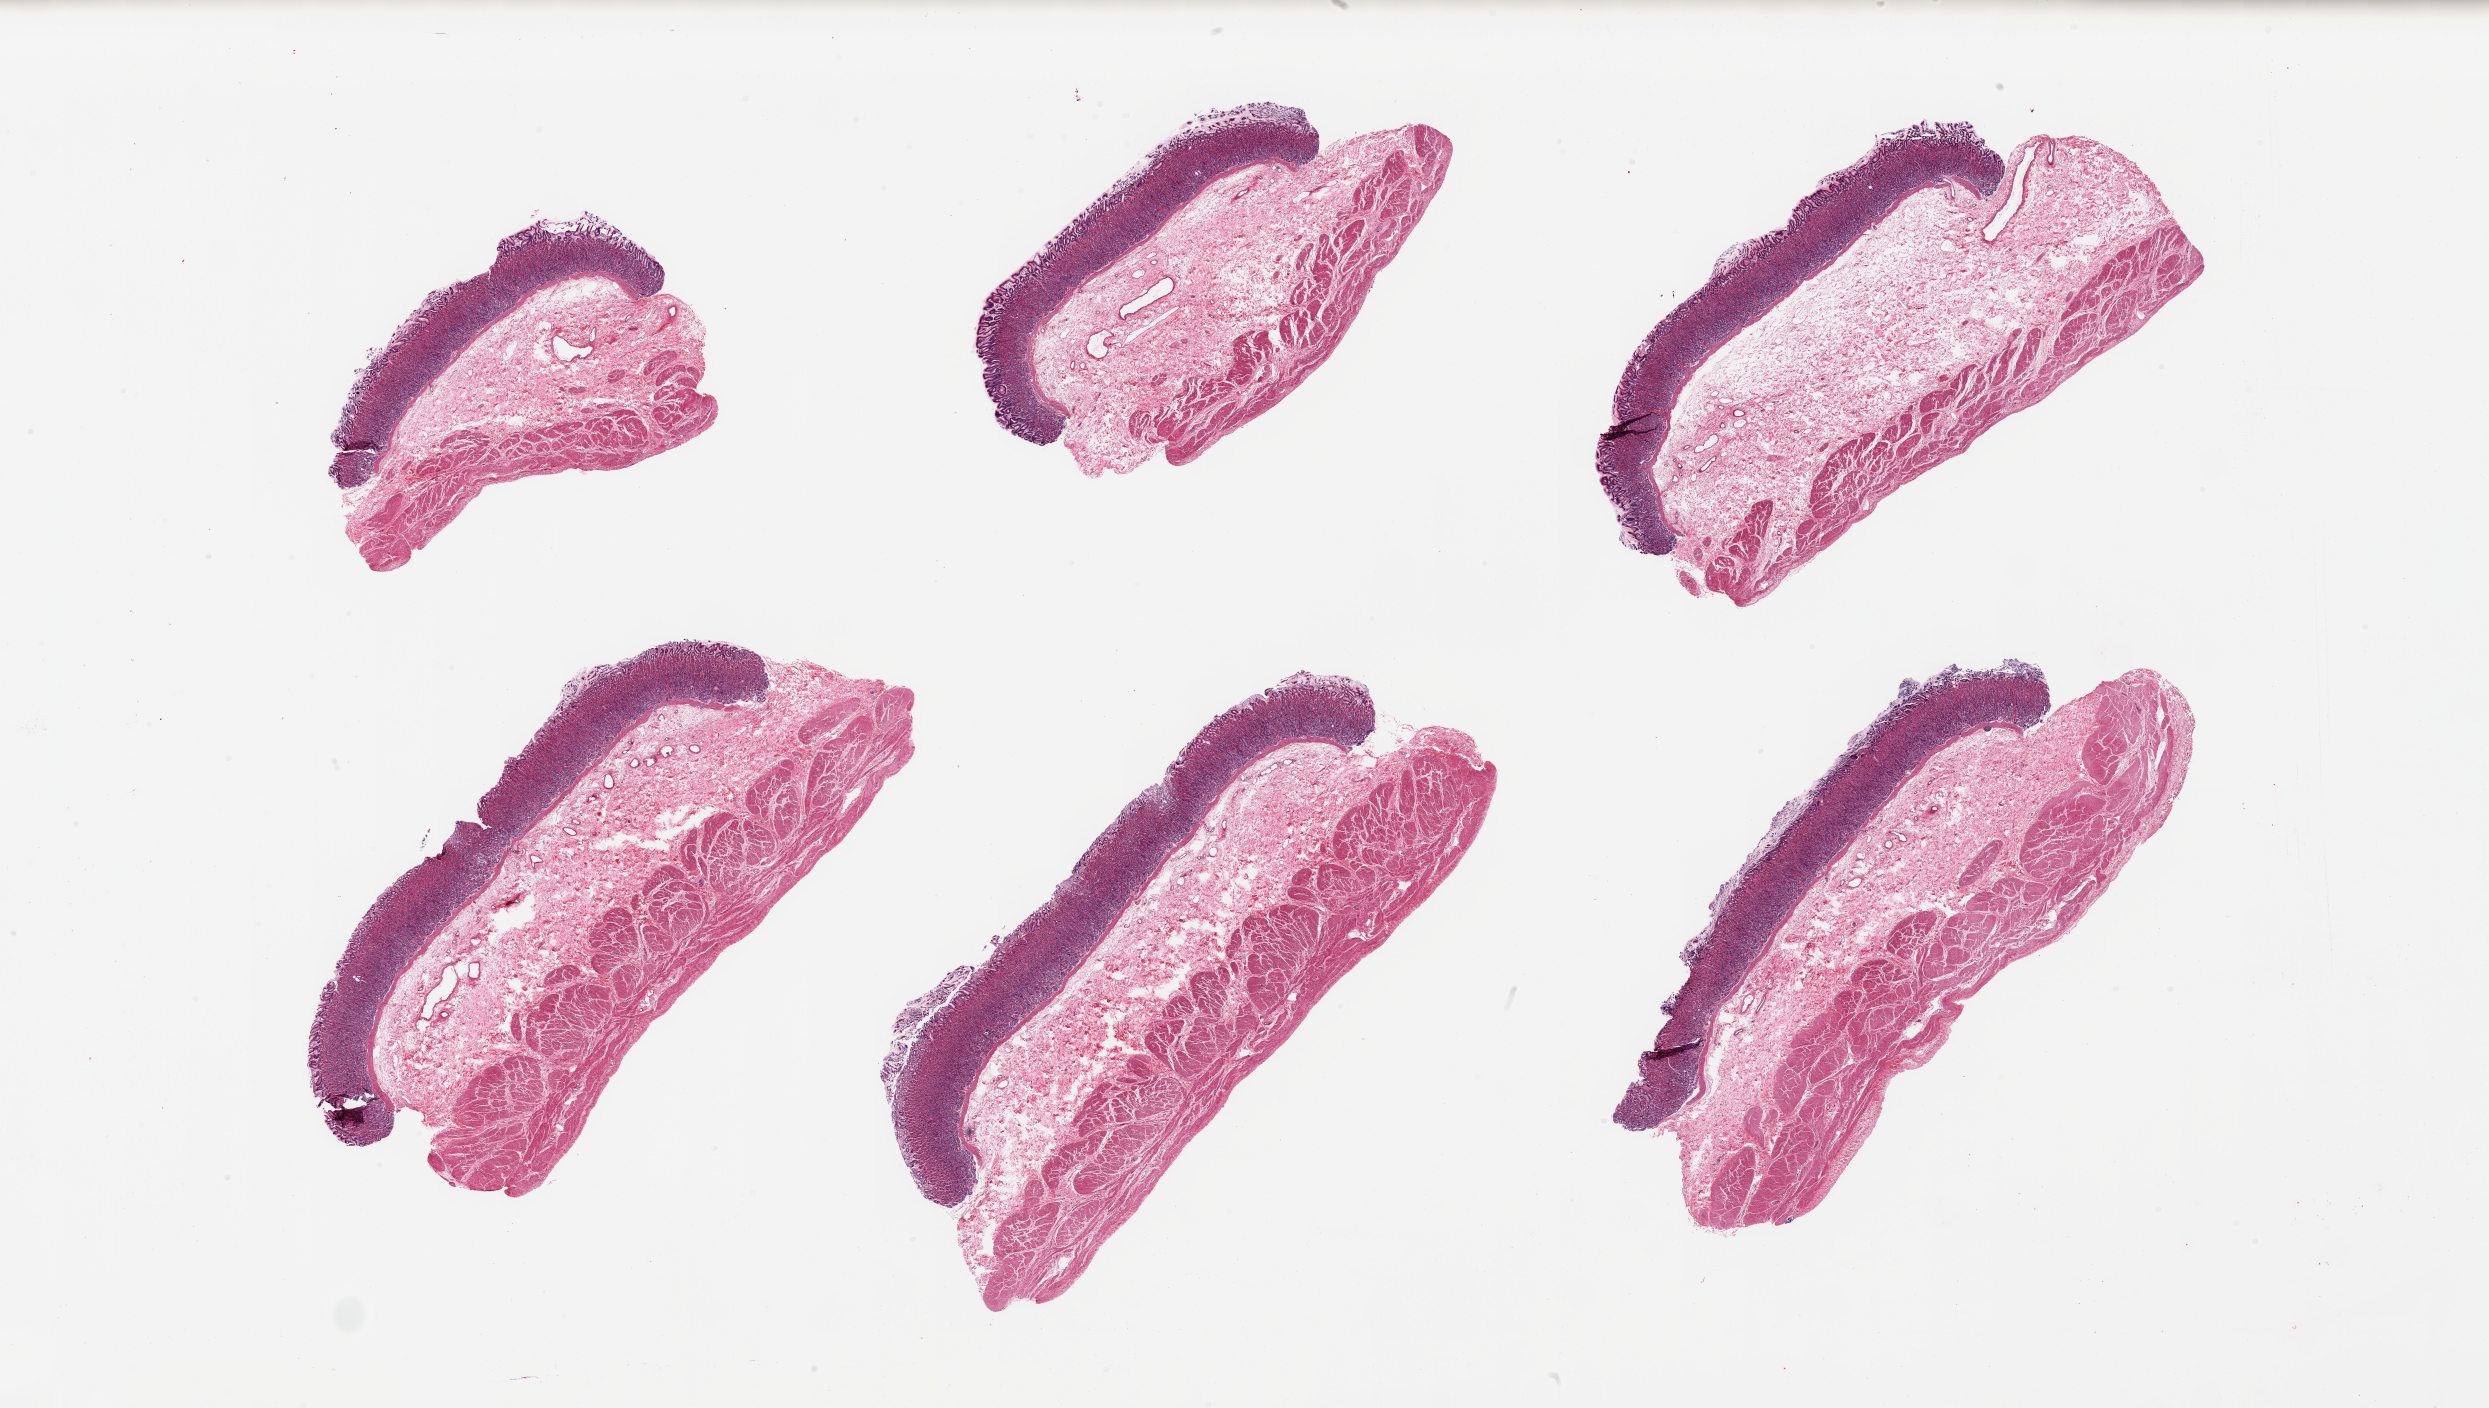
Whole-slide image, H&E stain, brightfield — whole scanned area (about 39.4 x 22.3 mm) shown as a low-resolution overview. PAXgene-fixed paraffin-embedded (PFPE) section. Section of stomach (target tissue). Tissue donor sample.
Pathologist's review note for this sample: 6 pieces; full thickness sections, well preserved, foveolar surface partly sloughed.